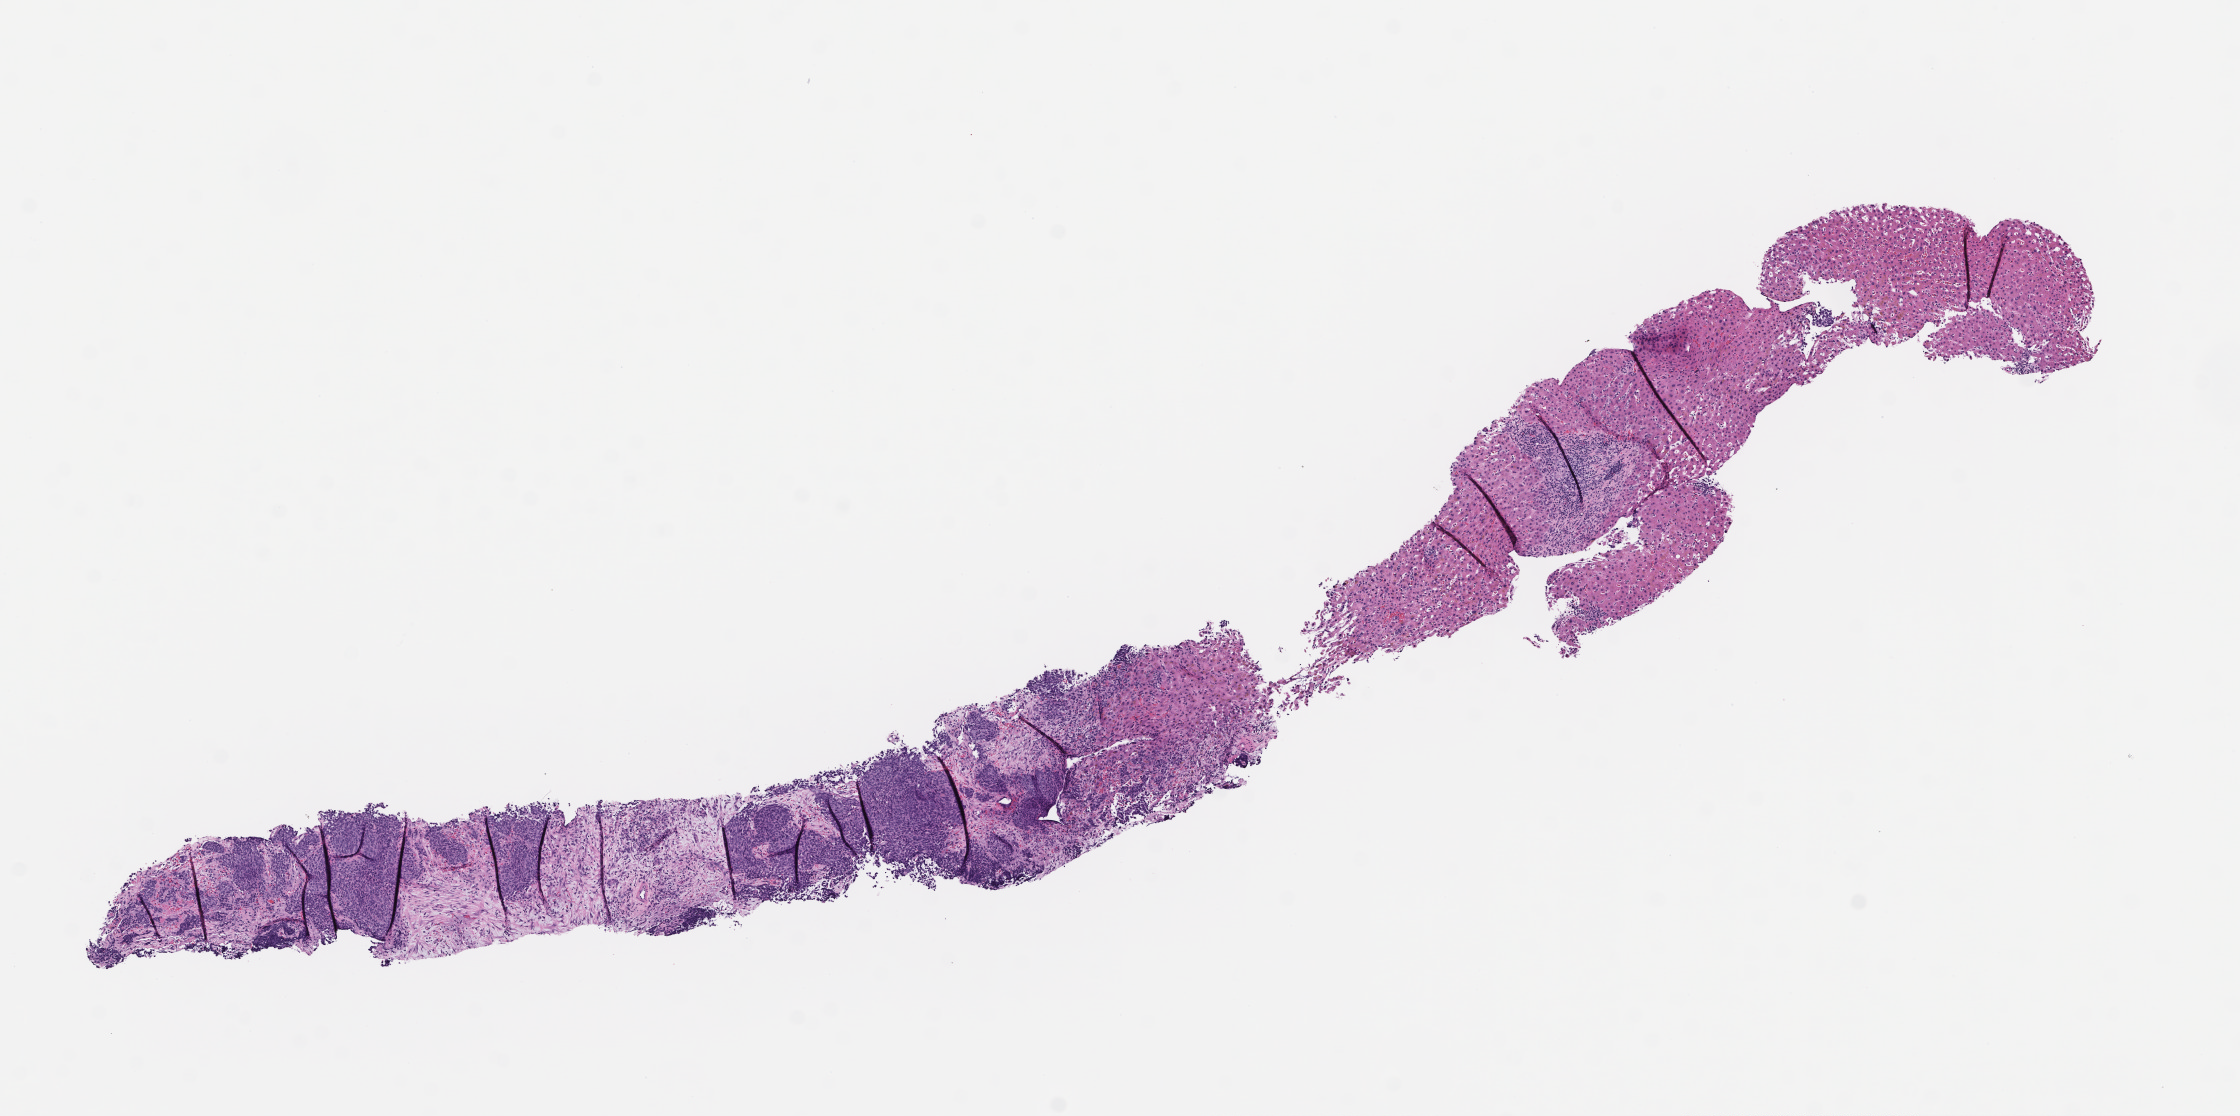
Whole-slide image, haematoxylin and eosin stain, a low-resolution overview of the entire scanned area, about 9.0 x 4.5 mm. Formalin-fixed, paraffin-embedded (FFPE) tissue. Specimen time point: collected at disease progression. Patient sex: female.
This section: metastatic tumor tissue. Patient diagnosis (primary): Non-Small Cell Lung Carcinoma.